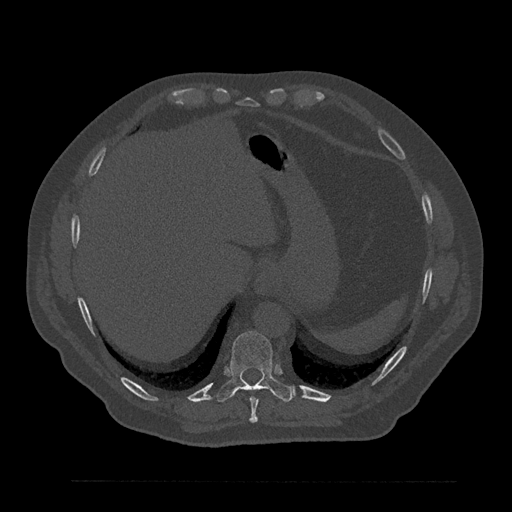
CT including the spine, one axial slice; position 365 of 797 along the scan axis; 120 kVp; bone window (W 1800 / L 400 HU); 0.5 mm slice thickness; 512 × 512 image matrix, field of view 430 × 430 mm. Male patient, age 61 years. From the clinical record (not read from this slice): primary cancer: prostate.
Structures marked on this image (semi-automatically segmented with operator editing):
- T10 vertebra: bounding box [x1, y1, x2, y2] px = [216, 331, 294, 402]
- T9 vertebra: [249, 397, 259, 423]